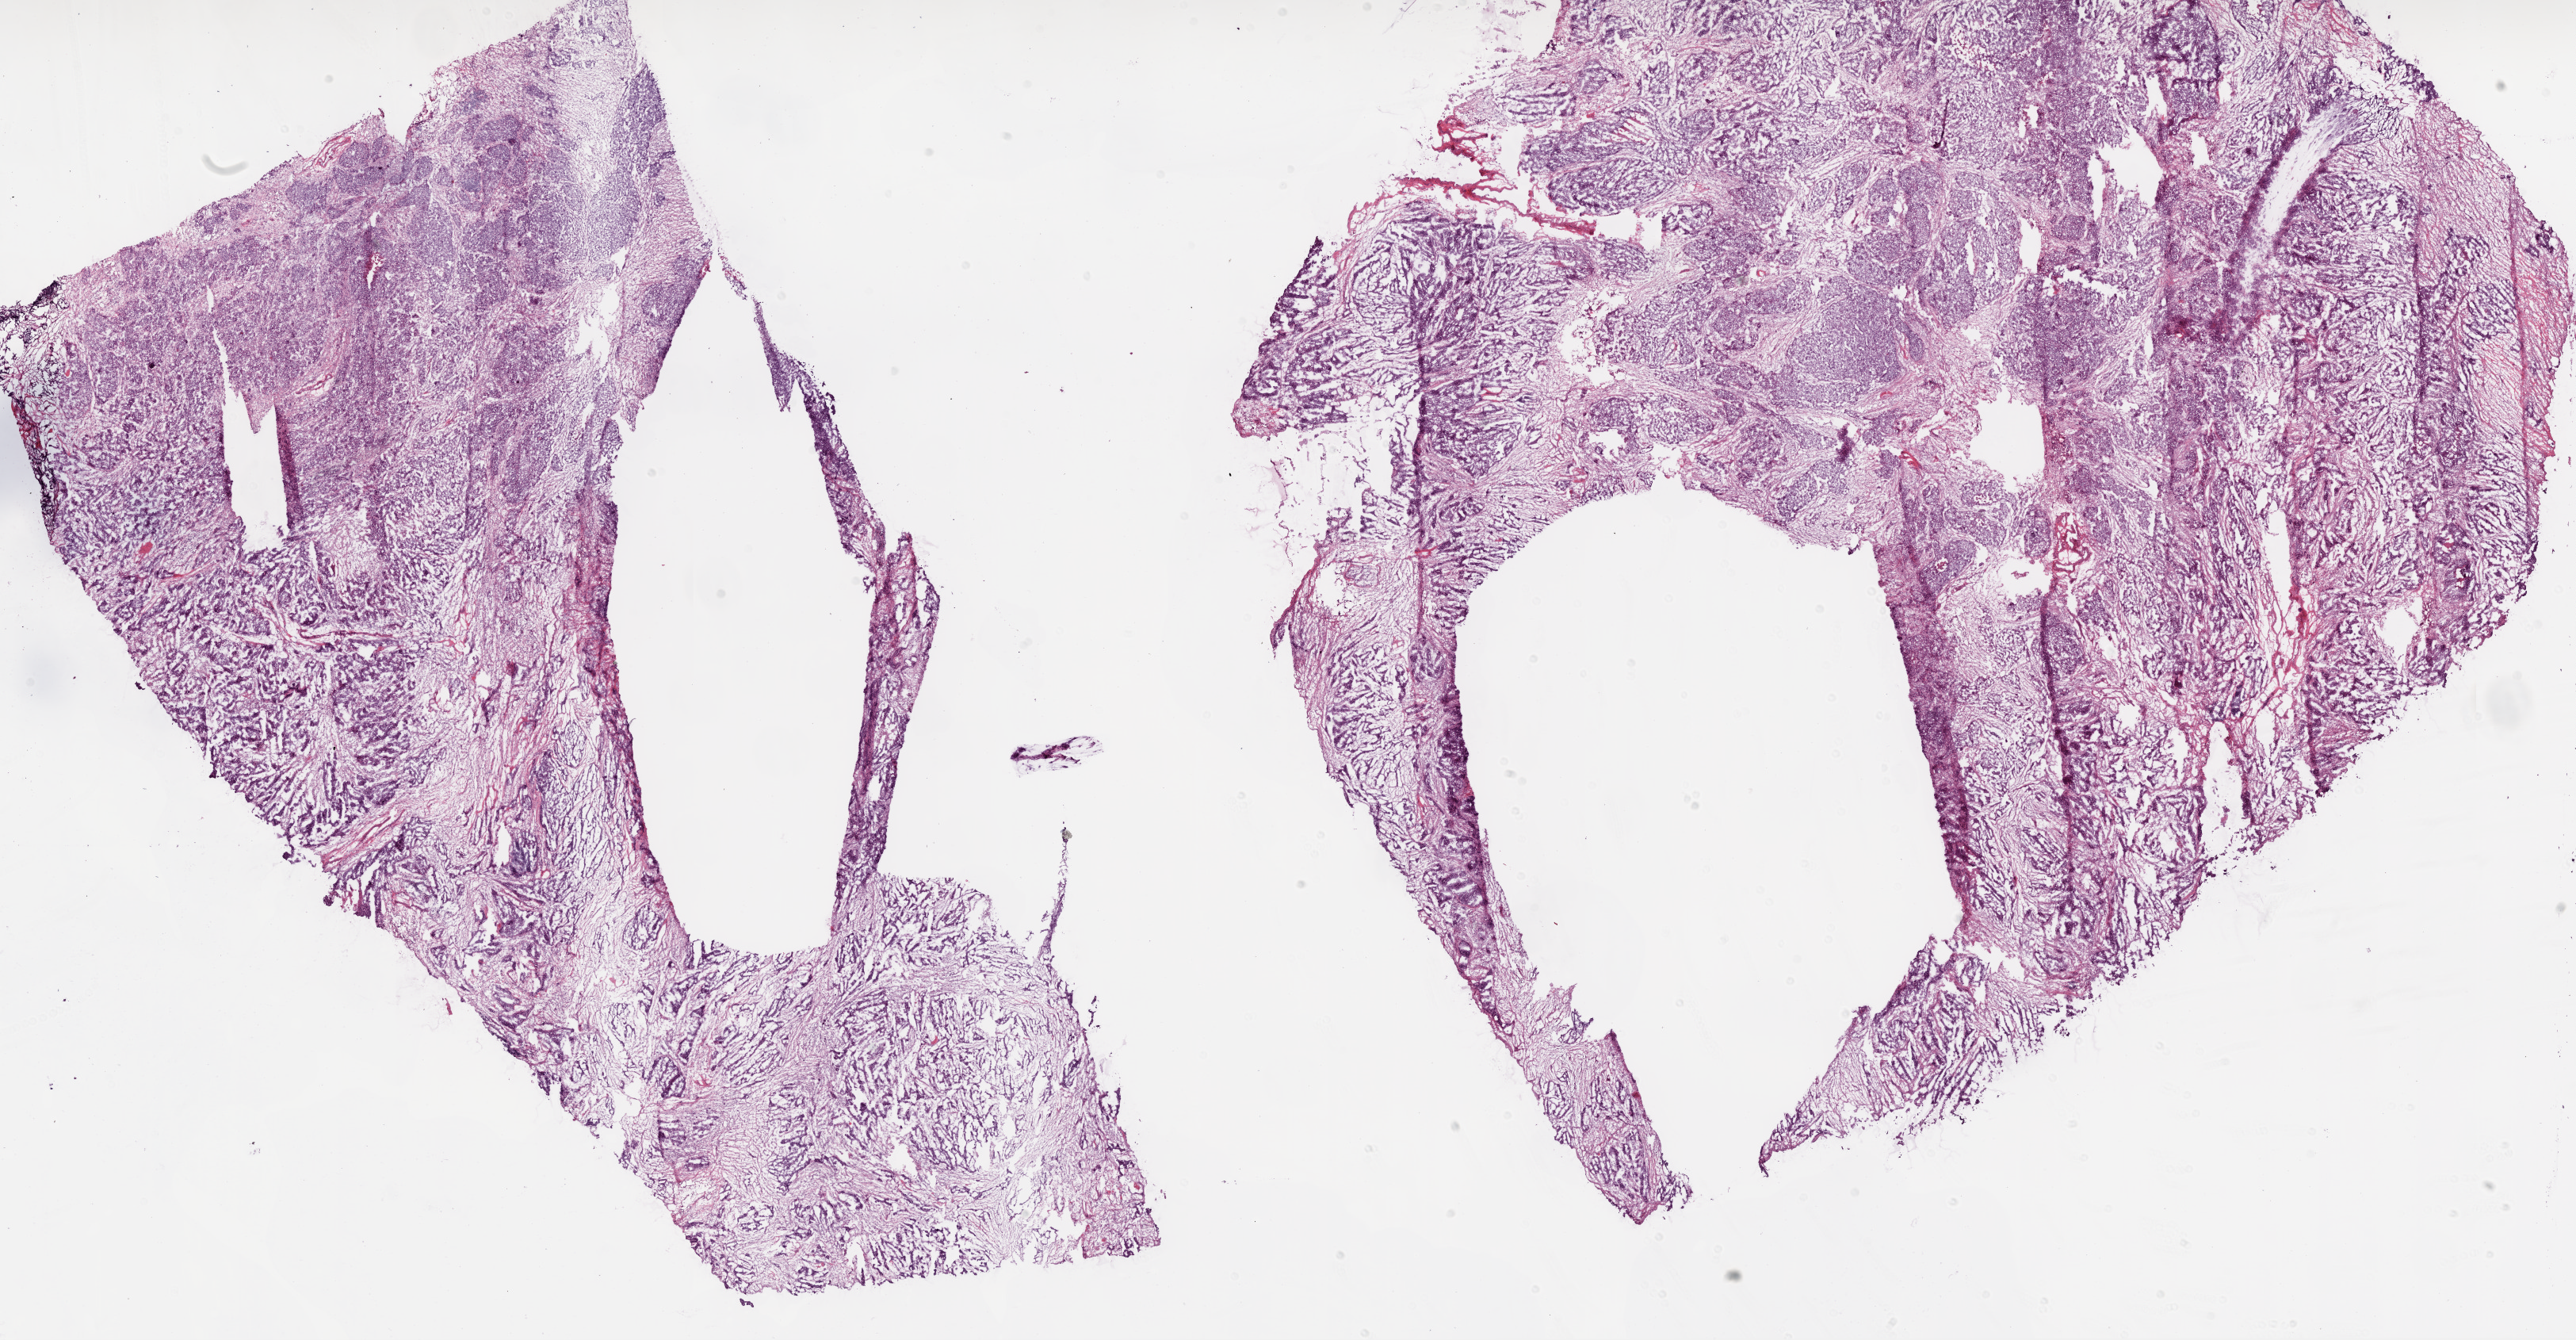
Whole-slide histology image, Hematoxylin and eosin (H&E) stained, a low-resolution overview of the entire scanned area, about 26.1 x 13.6 mm. Frozen section from the bottom of the tissue portion. Sample: primary tumour, ovary. Female, age 71 years at initial diagnosis. Histologic grade: G3 (poorly differentiated). Slide review estimates, as recorded: tumour cells 89%, tumour nuclei 90%, normal cells 0%, stromal cells 10%, necrosis 1%.
FIGO stage: IIIC. Diagnosis: Serous cystadenocarcinoma, NOS.